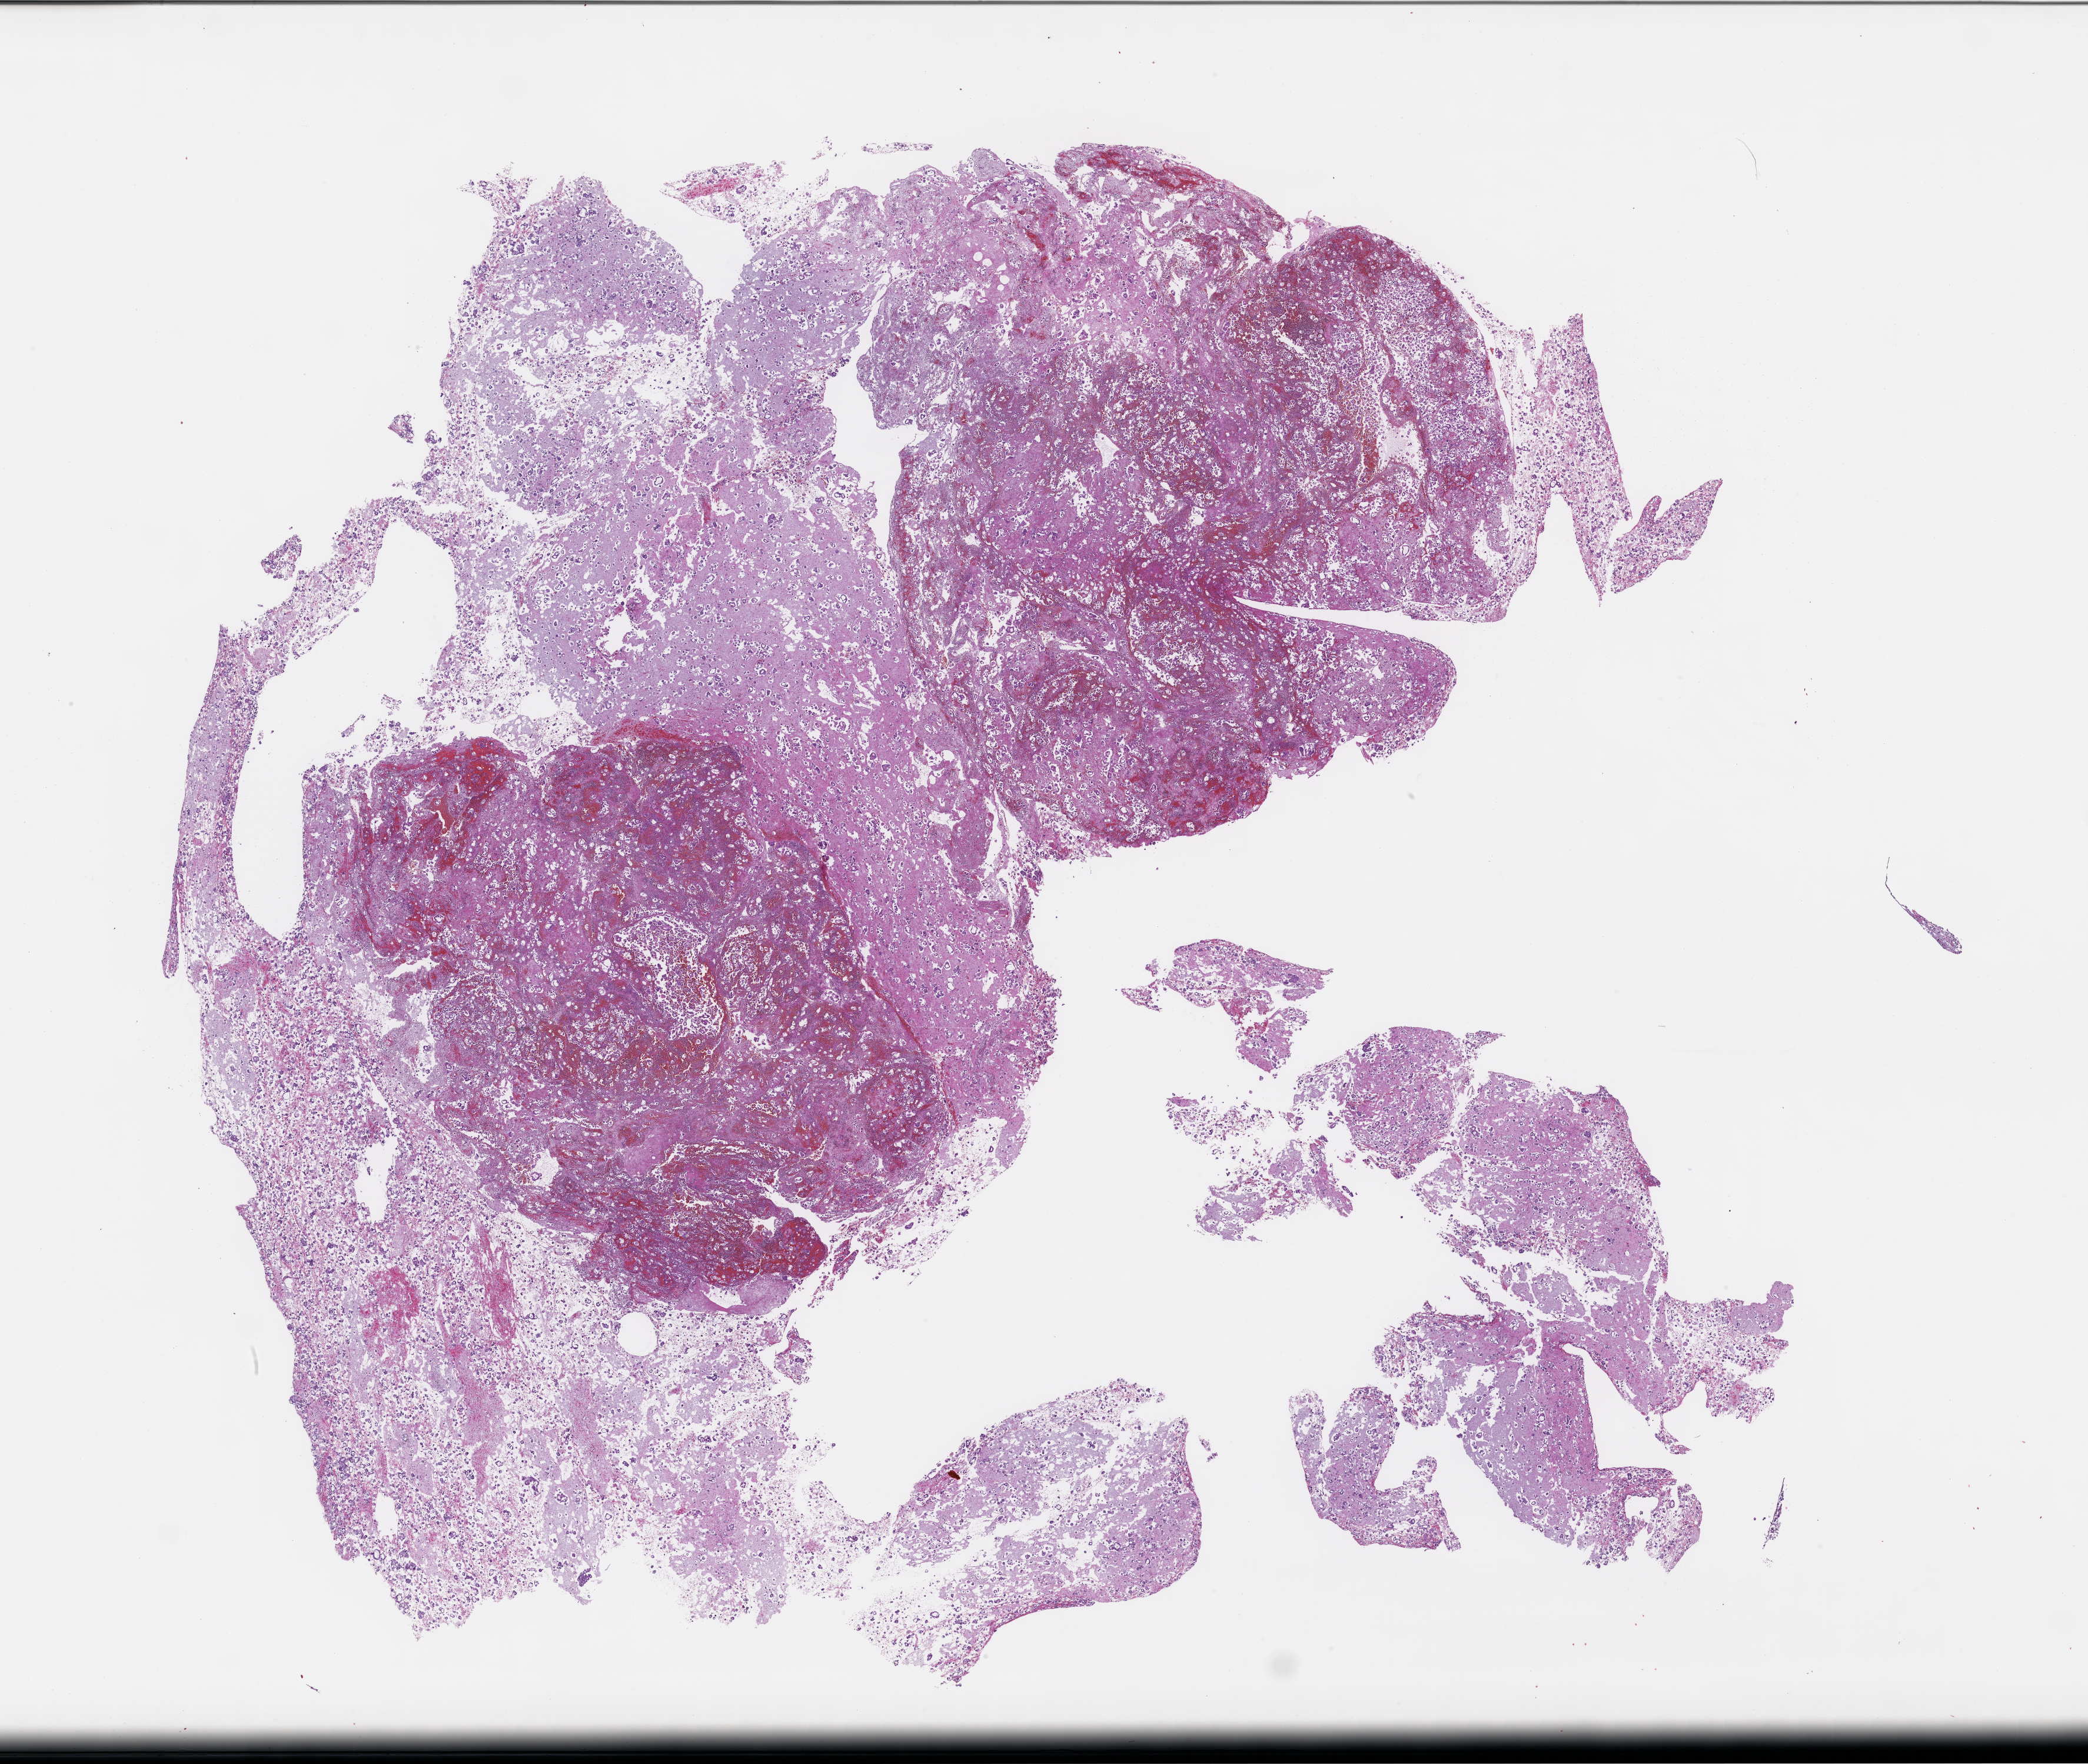
Digitized haematoxylin and eosin-stained section — a low-resolution overview of the entire scanned area, about 28.6 x 24.2 mm. Formalin-fixed paraffin-embedded section. Site: lung. Patient sex: male.
* this section: primary tumor
* diagnosis: Non-Small Cell Lung Carcinoma